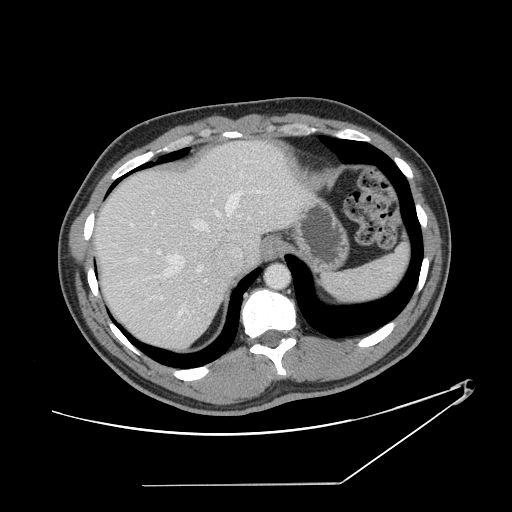
Contrast-enhanced abdominal CT, one axial slice. Slice 117 of 152 in the series (ordered by position). Reconstruction kernel STANDARD. 120 kVp. Intravenous contrast given. Soft-tissue window (W 400 / L 40 HU). 2.5 mm slice thickness. 512 × 512 image matrix, field of view 432 × 432 mm. Male patient, age 45 years. From the clinical record (not read from this slice): diagnosis: colorectal cancer liver metastases, imaged before liver resection; multiple liver metastases: no.
Structures marked on this image (manually delineated by an expert):
- hepatic veins: bounding box <111,189,266,314> (left, top, right, bottom; pixels)
- liver: <97,142,305,349>
- planned liver remnant (the part of the liver to remain after resection): <97,164,233,350>
- portal vein (with intrahepatic branches): <157,251,208,326>